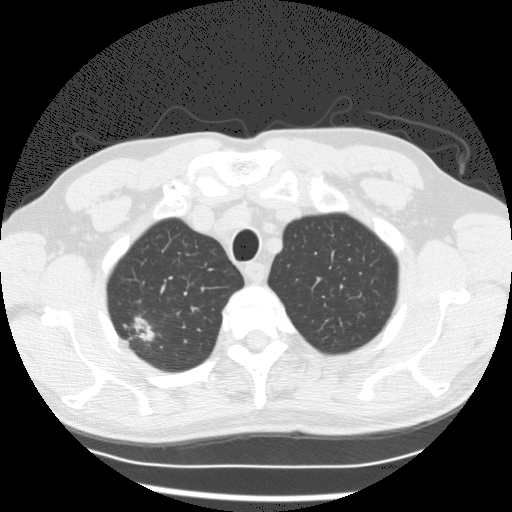
Low-dose screening chest CT, one axial slice. Slice 112 of 132 in the series (ordered by position). Reconstruction kernel STANDARD. 120 kVp. Lung window (W 1500 / L -600 HU). 2.5 mm slice thickness. 512 × 512 image matrix, field of view 351 × 351 mm.
Structures marked on this image (expert manual segmentation):
- lesion 1 (tumor, upper lobe of right lung): bounding box <138,329,155,342> (left, top, right, bottom; pixels)